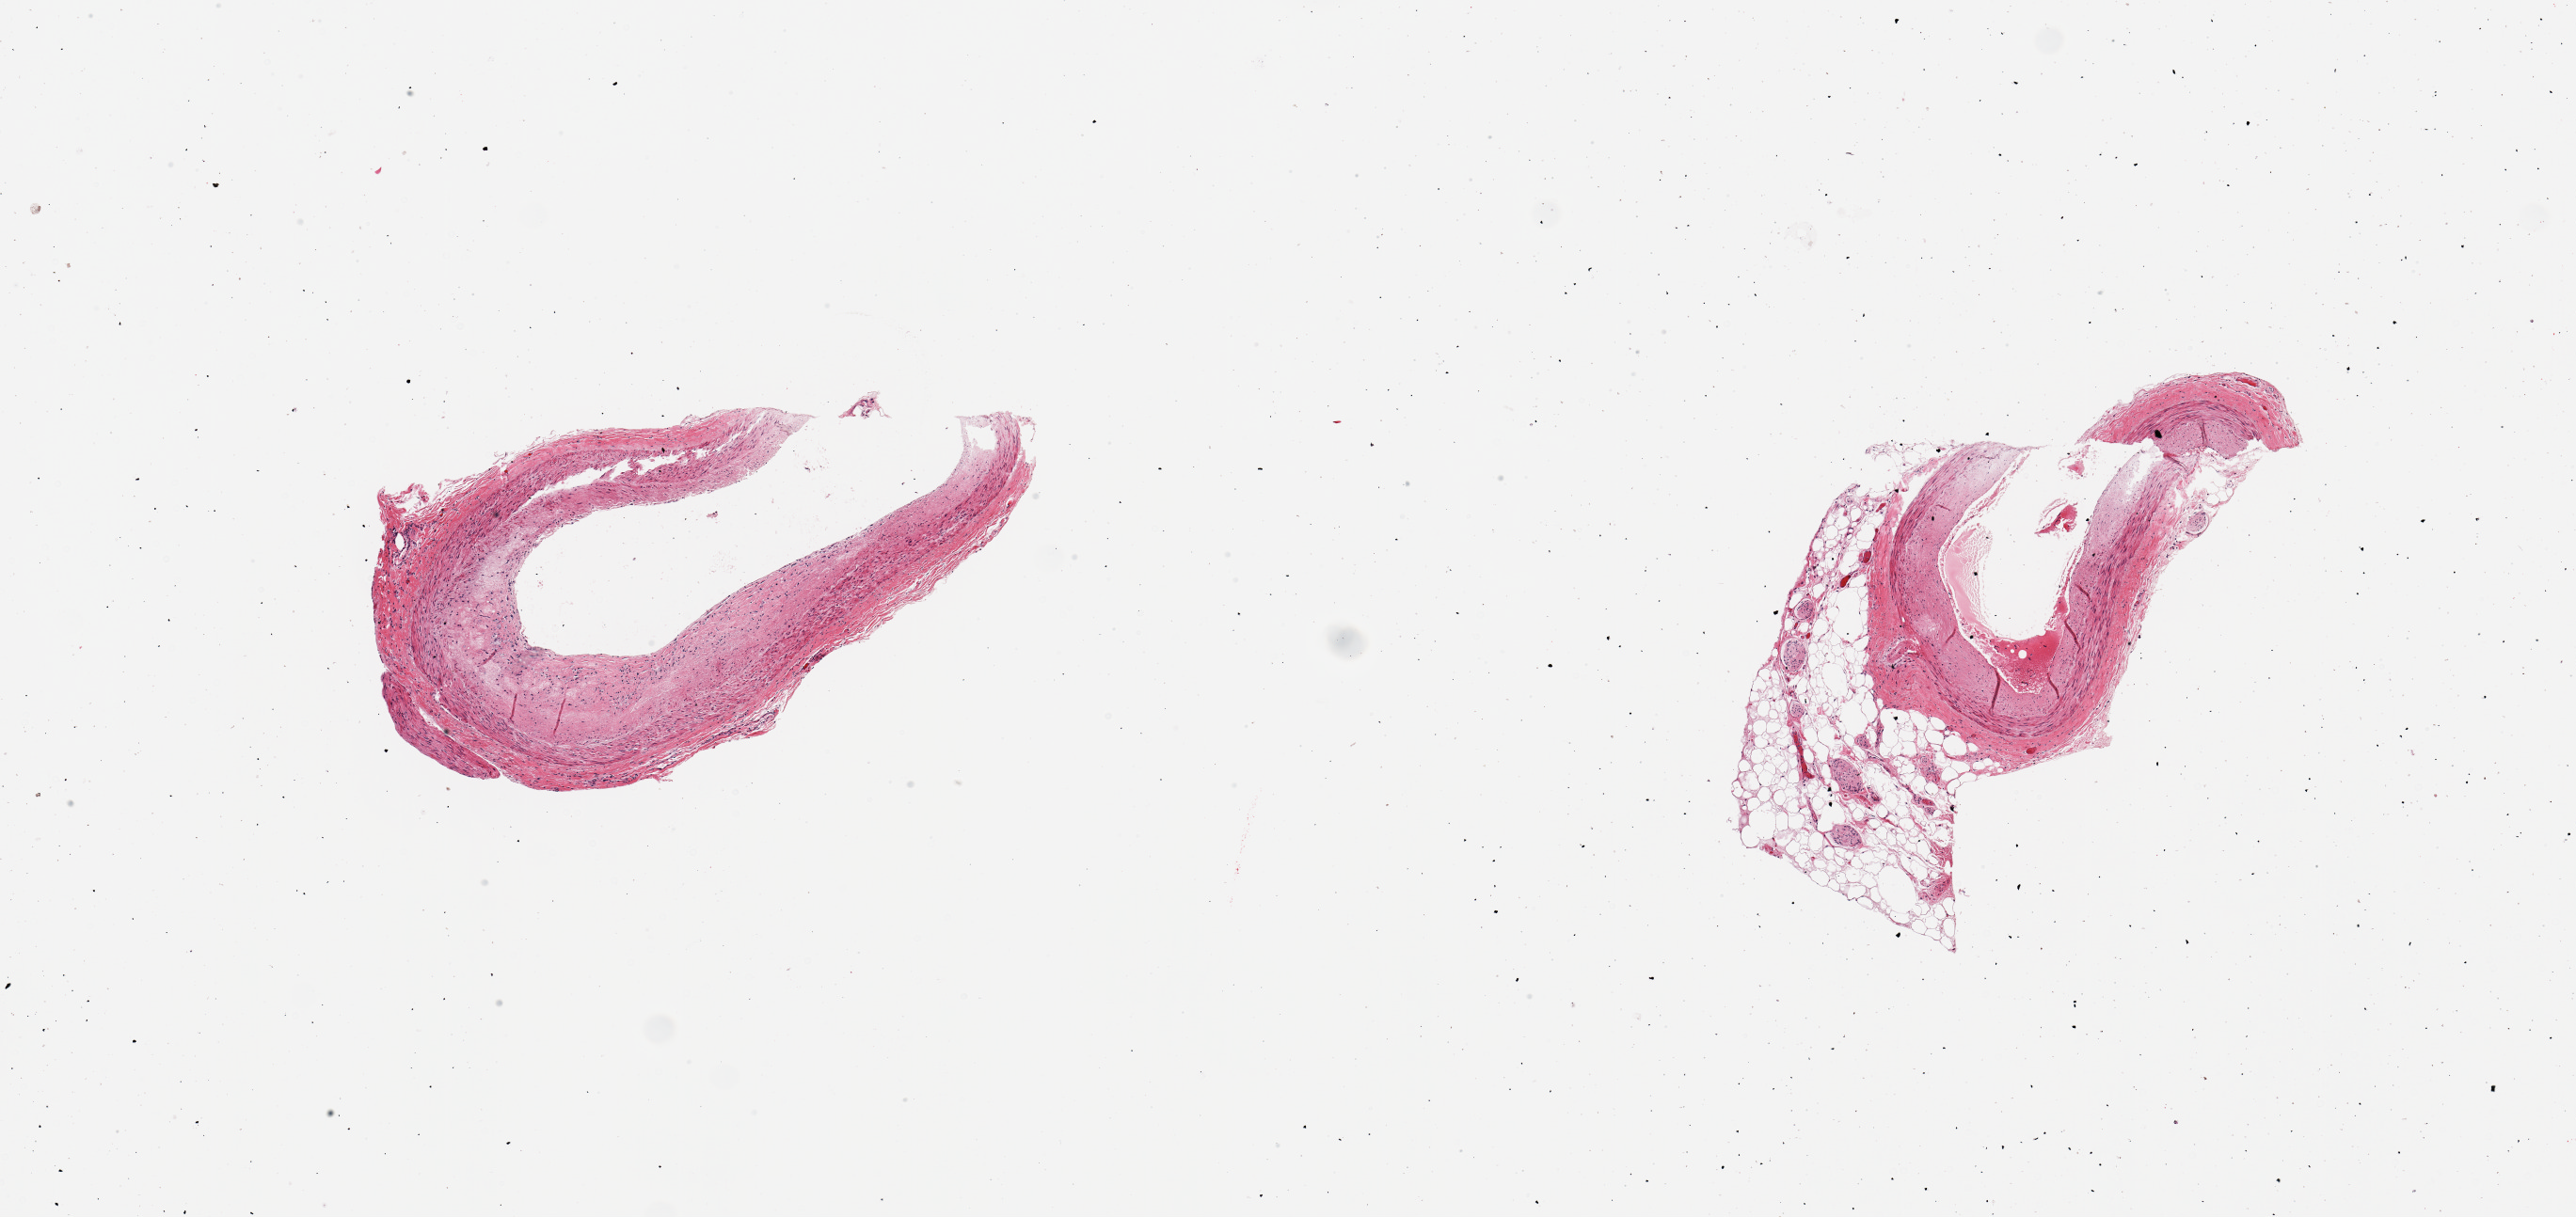
Digitized H&E-stained section, low-resolution overview of the scanned area, about 10.8 x 5.1 mm (slide scanned at 20x); PAXgene-fixed, paraffin-embedded tissue; target tissue: coronary artery; donor tissue sample.
• reviewer comment on this tissue sample: 2 pieces; moderate plaque; 50% external fat on 1